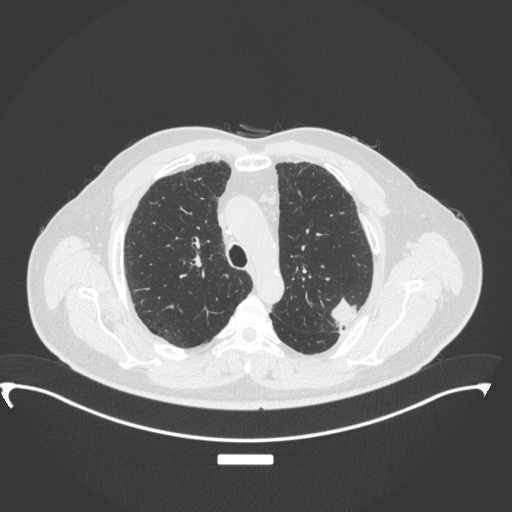
Chest CT, one axial slice. Position 261 of 350 along the scan axis. 120 kVp. Lung window (W 1500 / L -600 HU). 1 mm slice thickness. 512 × 512 image matrix, field of view 459 × 459 mm. Patient: male, 64 years. From the clinical record (not read from this slice): clinical TNM (as recorded): T1c N1 M1.
Annotated regions visible in this slice (rectangle marked by the reading radiologist):
- lung tumour (recorded histology: adenocarcinoma): bounding box [x1, y1, x2, y2] px = [327, 294, 362, 330]